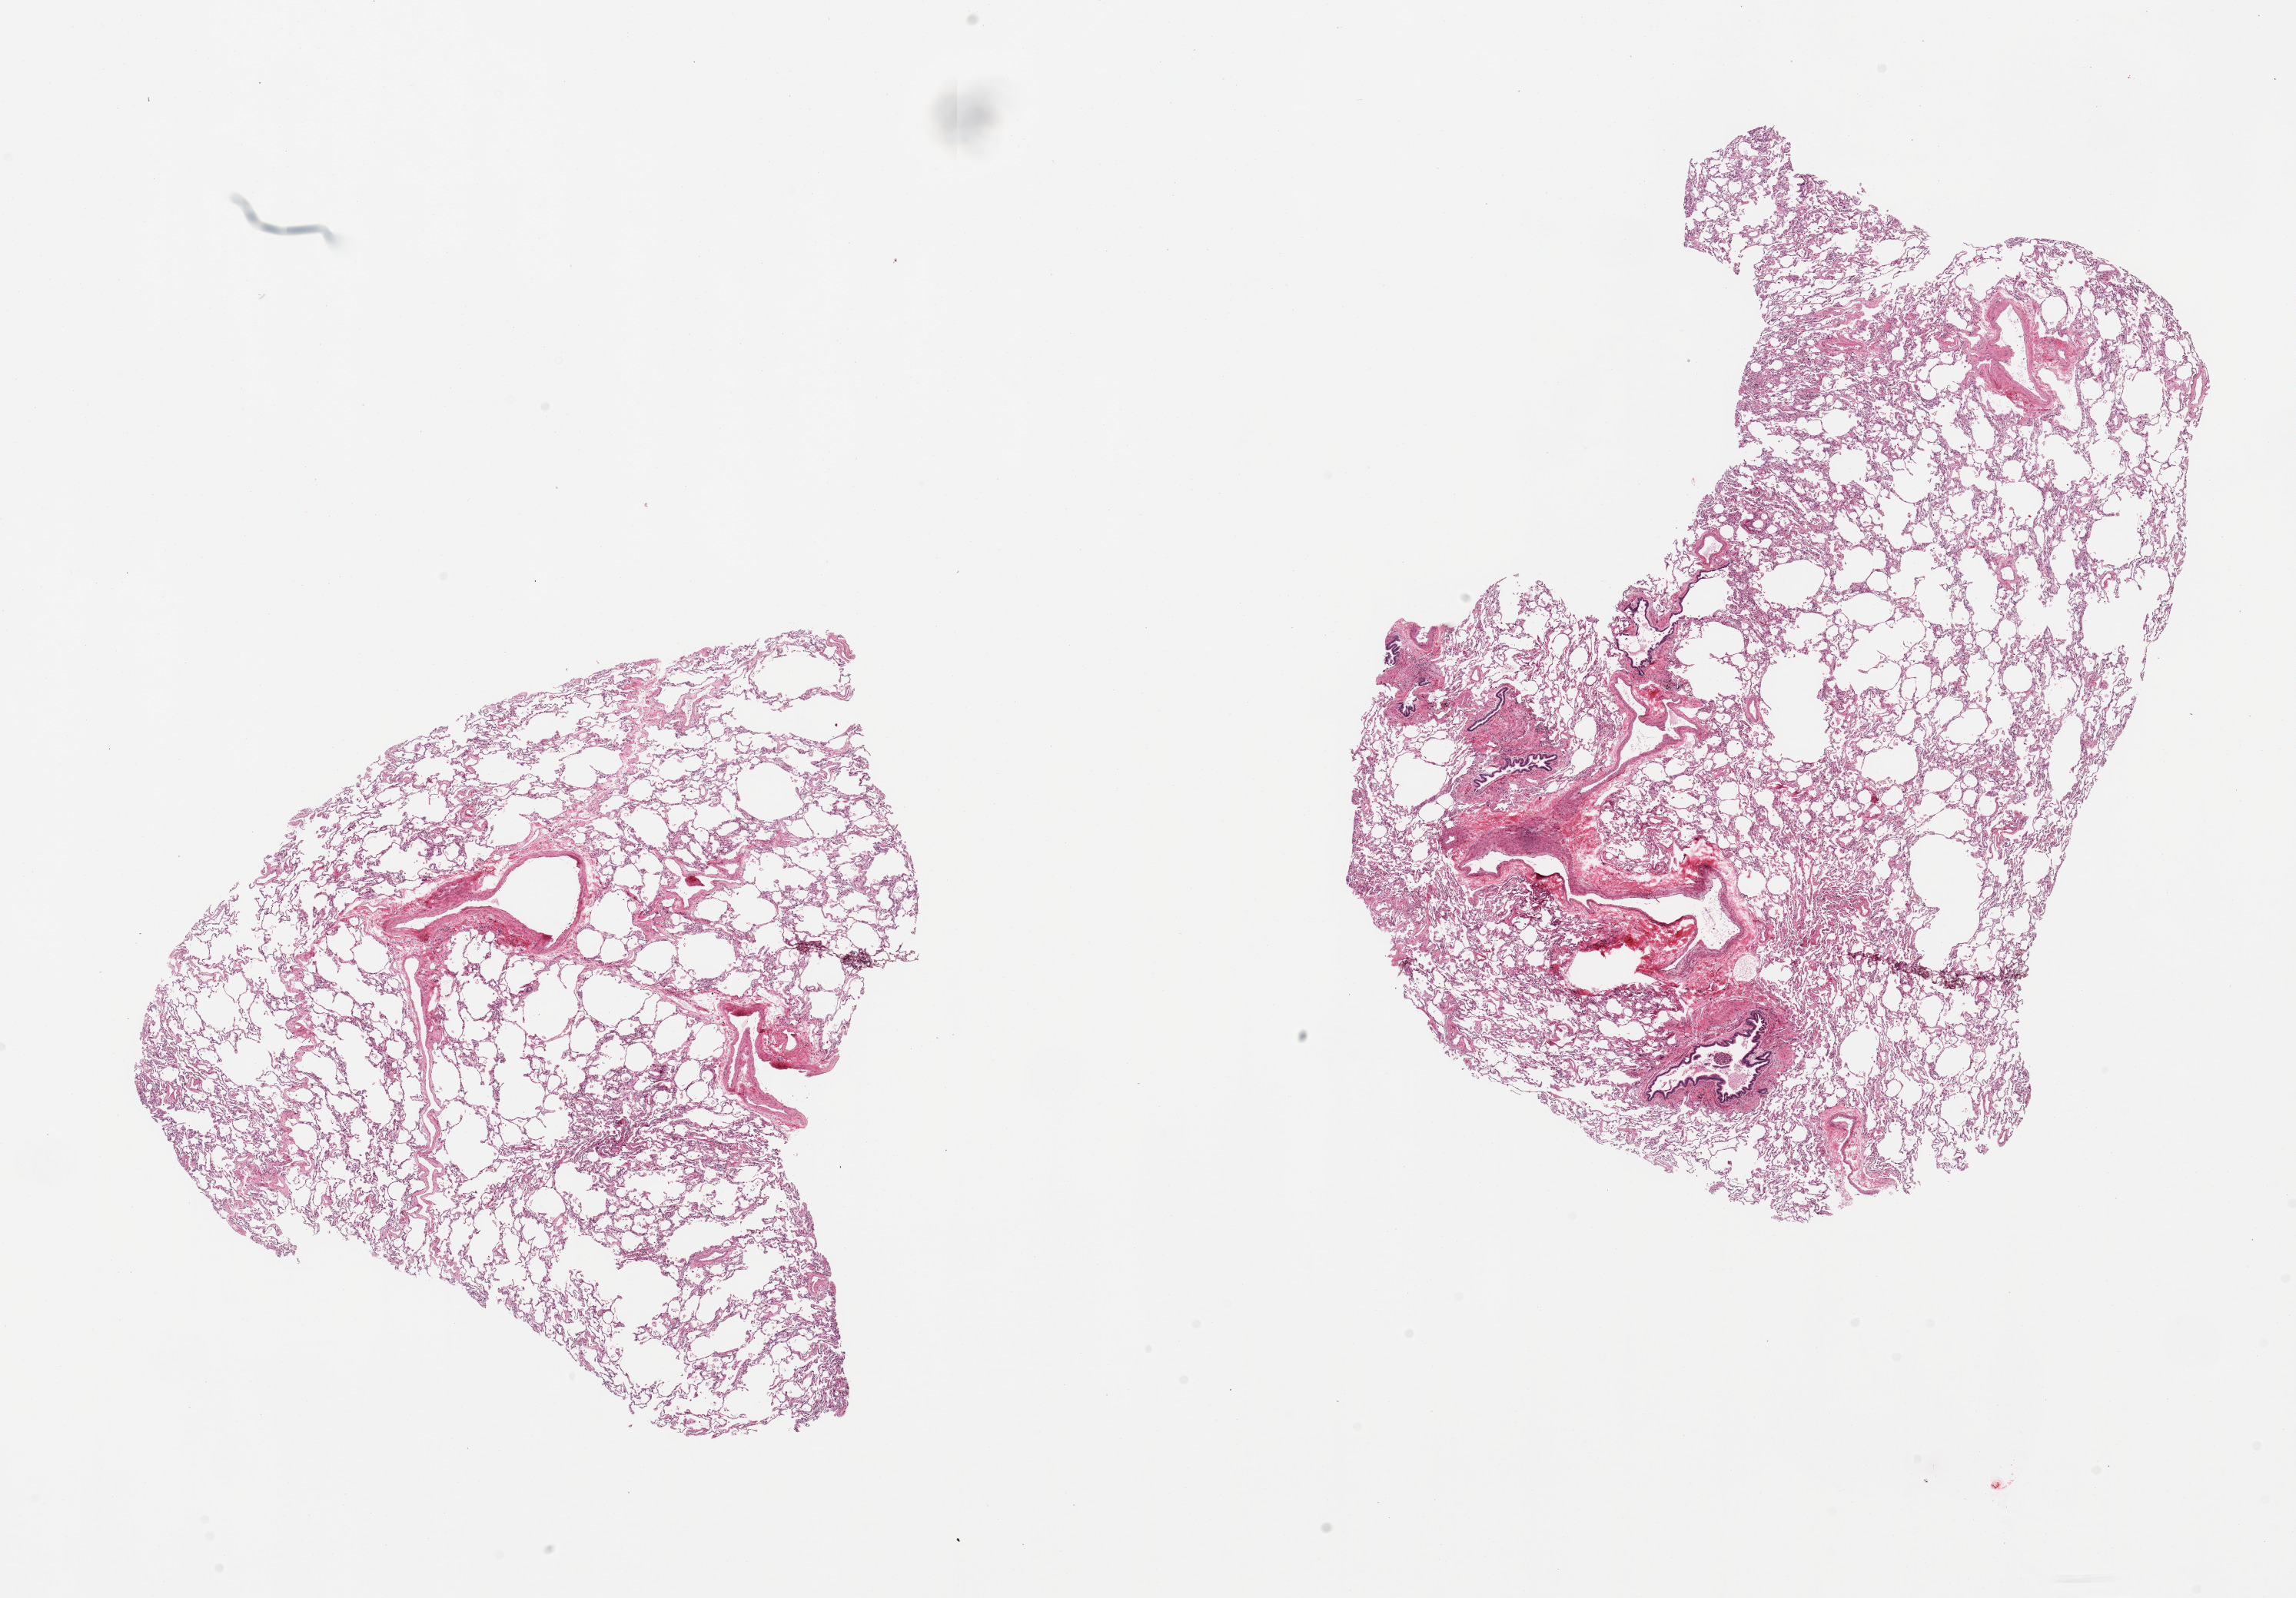
Whole-slide image, hematoxylin and eosin (H&E) stain — a low-resolution overview of the entire scanned area, about 23.6 x 16.4 mm (from a 20x scan). PAXgene-fixed, paraffin-embedded tissue. Target tissue: lung. Donor tissue sample. Male donor.
Review note (as recorded): 2 pieces; some widening of air spaces.